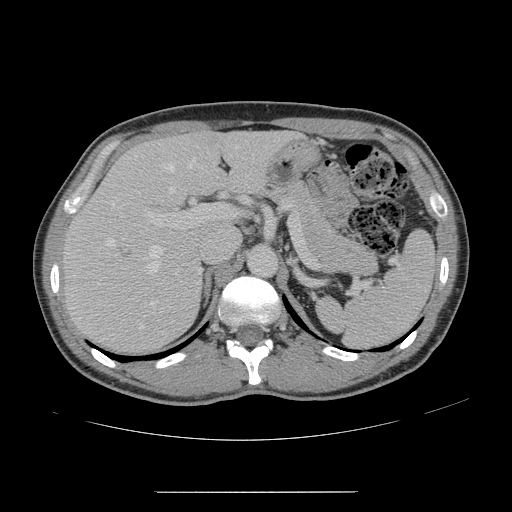
Contrast-enhanced abdominal CT, one axial slice. Slice 96 of 178 in the series (ordered by position). Soft-tissue window (W 400 / L 40 HU). 512 × 512 image matrix, field of view 401 × 401 mm. Male patient, age 53 years. From the clinical record (not read from this slice): diagnosis: colorectal cancer liver metastases, imaged before liver resection; multiple liver metastases: yes; largest metastasis: 2.4 cm; disease in both lobes: no.
Structures marked on this image (expert manual segmentation):
- hepatic veins: bounding box [x1, y1, x2, y2] px = [107, 145, 238, 328]
- liver: [65, 132, 293, 350]
- planned liver remnant (the part of the liver to remain after resection): [147, 132, 294, 193]
- portal vein (with intrahepatic branches): [145, 205, 233, 305]